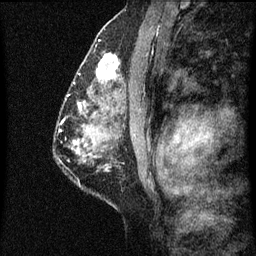
Breast MRI (dynamic contrast-enhanced), one sagittal slice; position 40 of 60 along the scan axis; dynamic contrast-enhanced series, image 2 of 7 at this slice position (ordered by acquisition); 1.5 T; TE 4.2 ms, TR 8 ms; 2 mm slice thickness; 256 × 256 image matrix, field of view 180 × 180 mm. Female patient, age 51 years.
Structures marked on this image (semi-automatically segmented with operator editing):
- analysis volume of interest (the breast-tissue region the enhancement analysis was run in; not a lesion): box from (x=86, y=50) to (x=125, y=101) px
- tumour enhancement mask (voxels above the 70 % enhancement threshold inside the analysis volume of interest): (x=98, y=54)–(x=119, y=83)